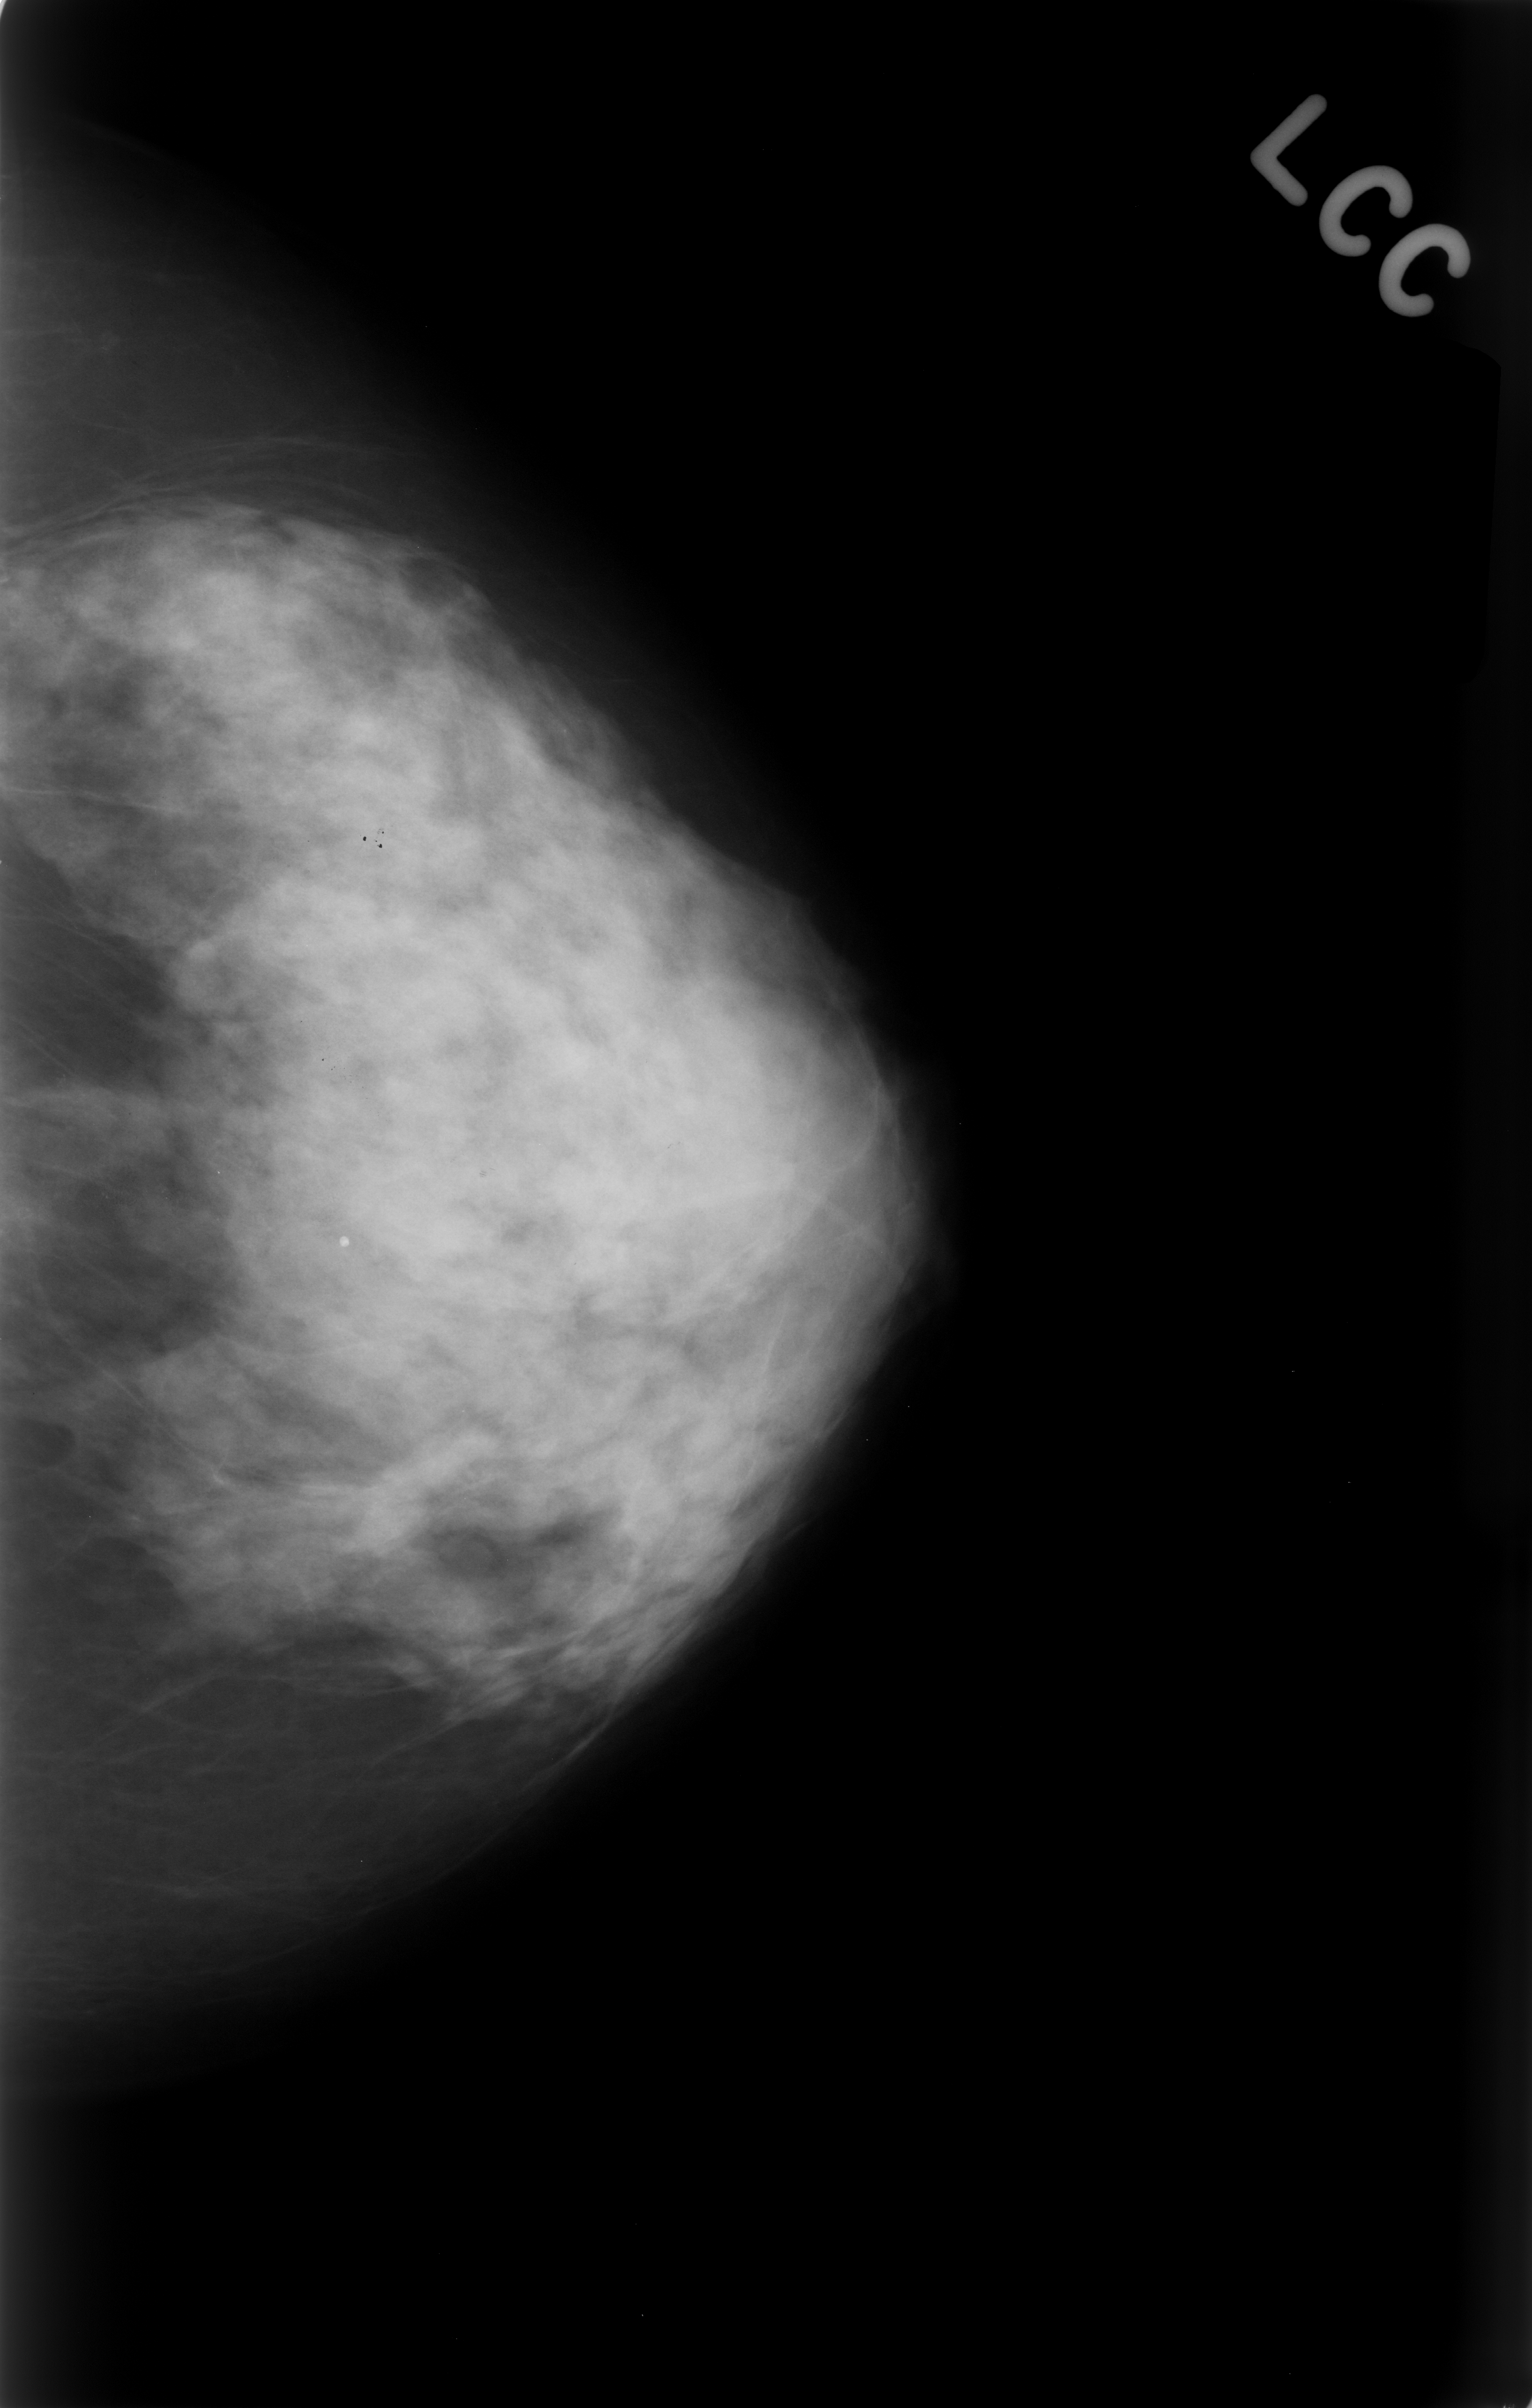
Mammogram (digitized film); left breast; CC view; breast composition: extremely dense (BI-RADS density category 4 of 4).
Marked findings (only marked abnormalities are described; nothing is implied about the rest of the image): calcifications, morphology amorphous, distribution segmental; BI-RADS assessment category 4; subtlety rating 2 on a 1 (subtle) to 5 (obvious) scale; pathology result (as recorded, not read from the image): benign.